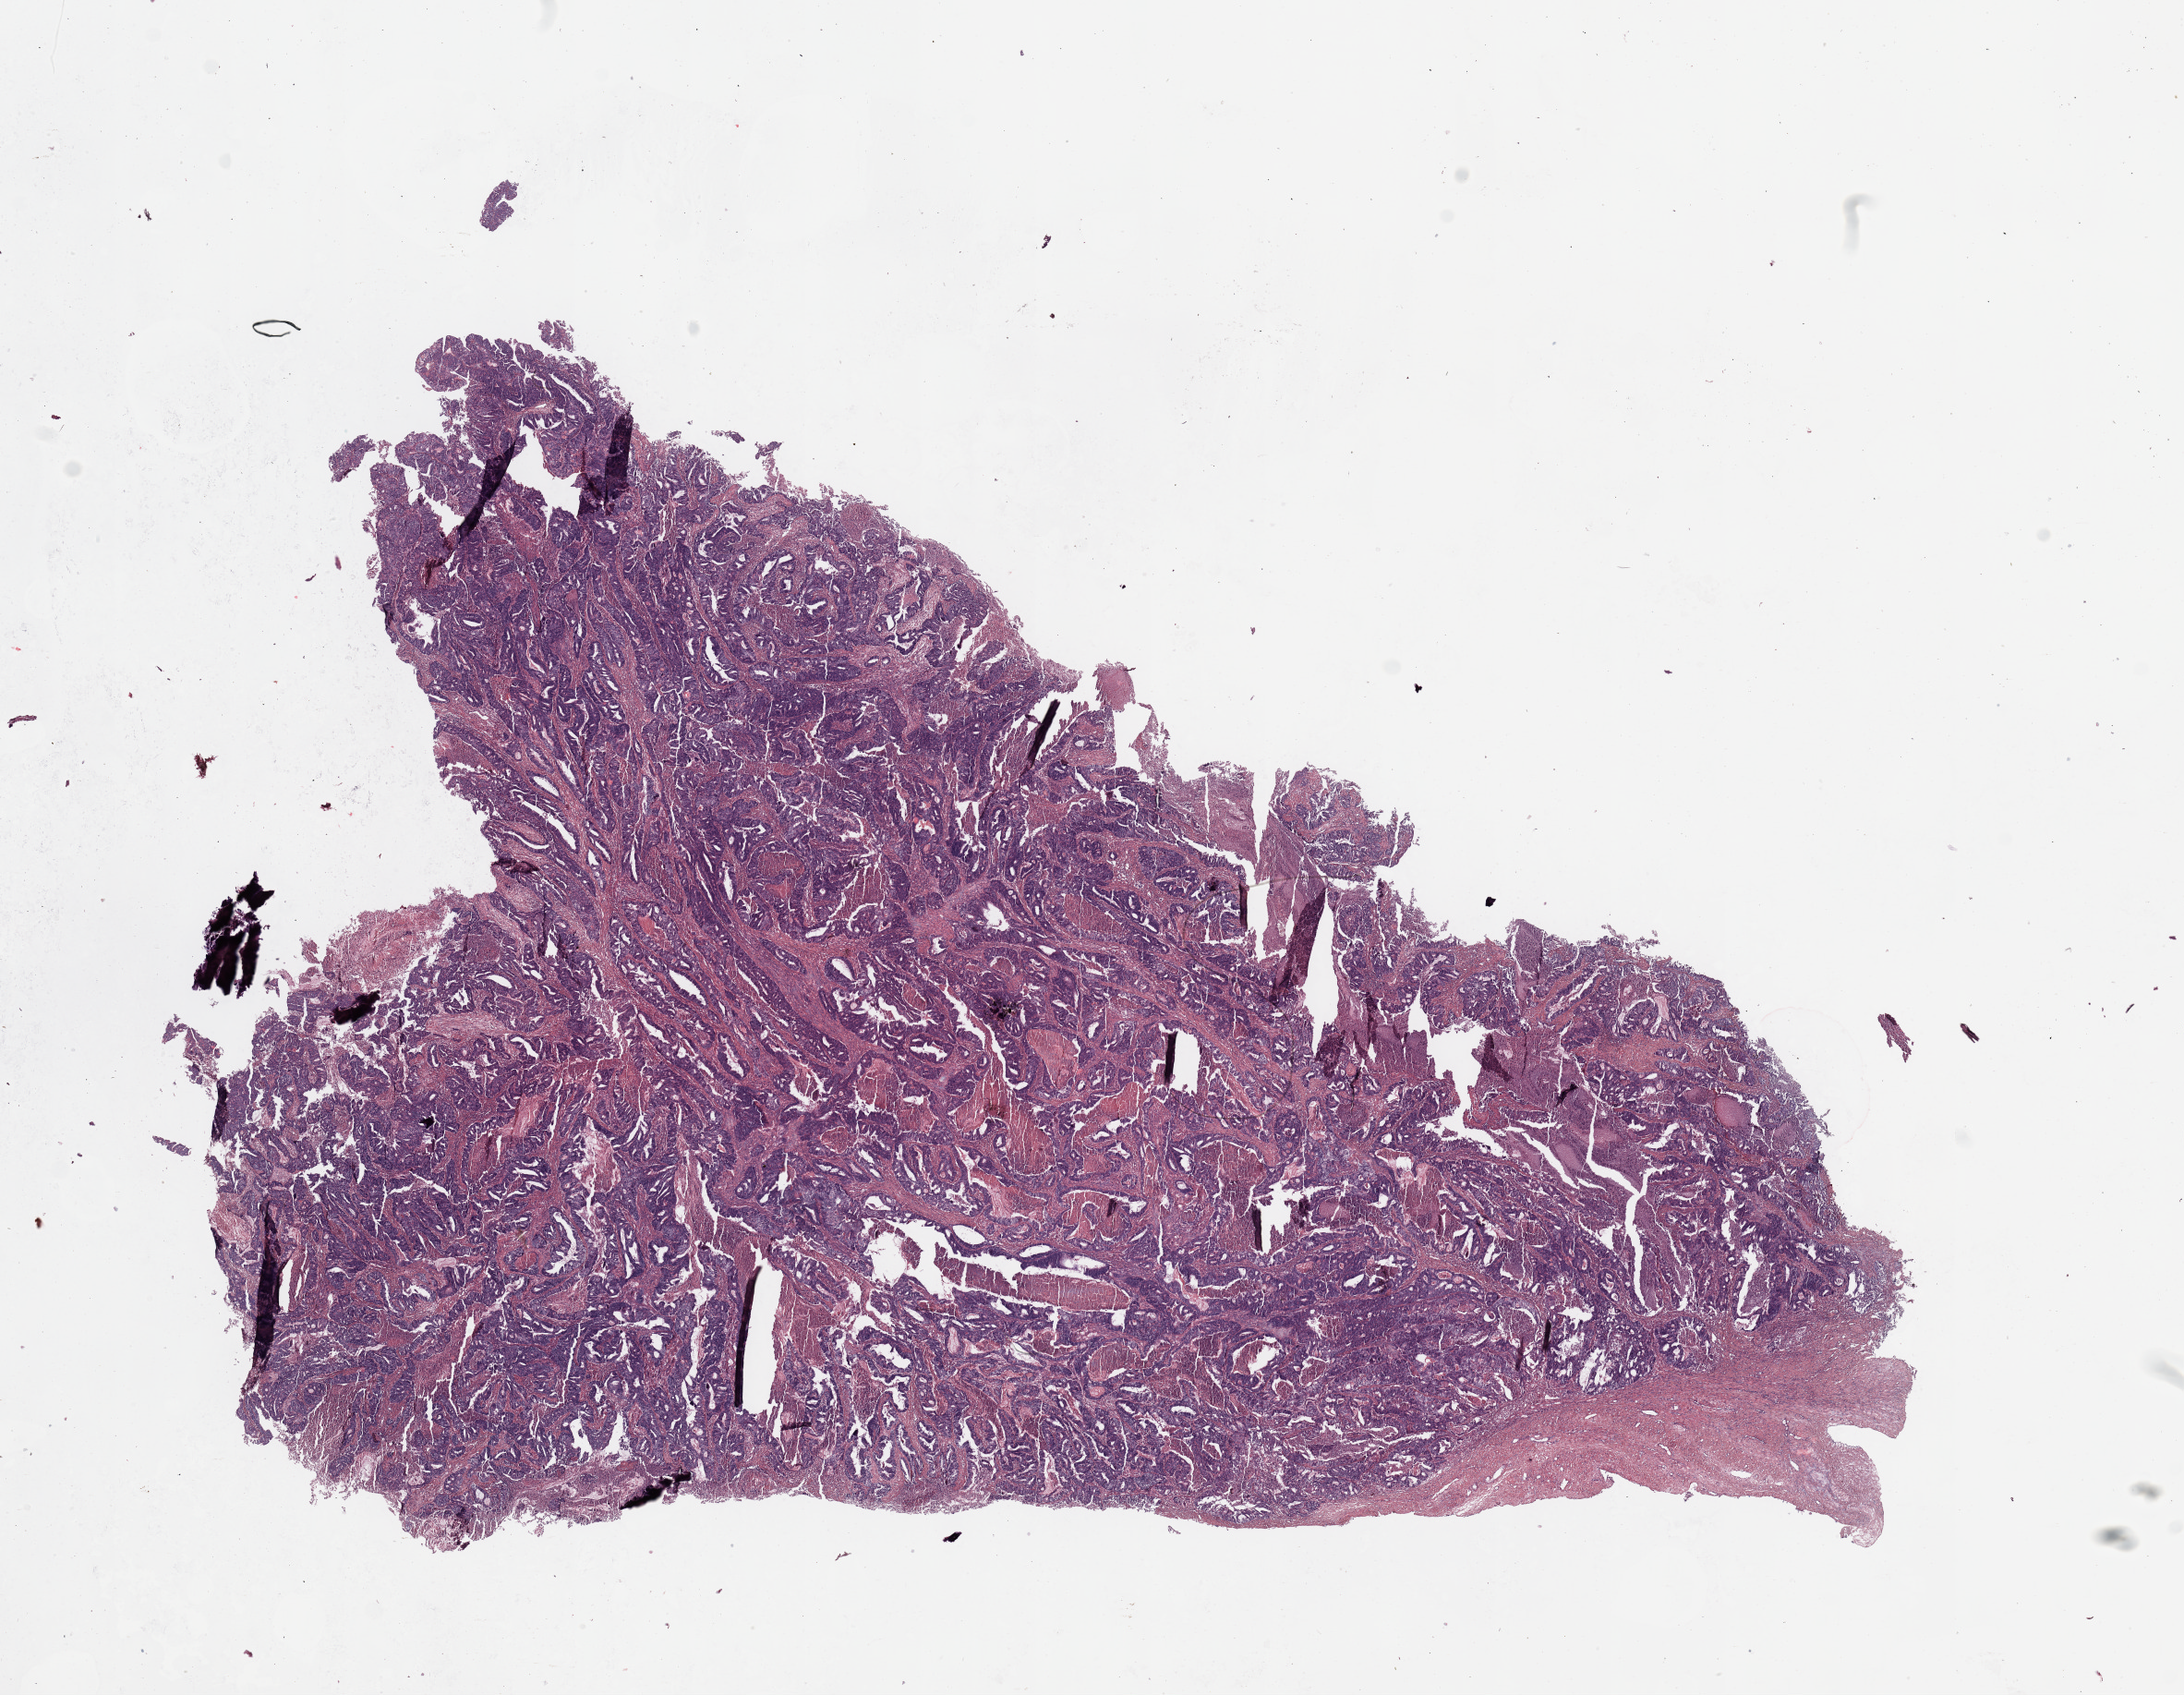
H&E-stained whole-slide image — whole scanned area (about 18.7 x 14.5 mm, slide scanned at 20x) shown as a low-resolution overview; tumour tissue sample, uterus. 62-year-old female patient. Histologic grade: G2 (moderately differentiated).
Diagnosis: Endometrioid adenocarcinoma, NOS. AJCC pathologic stage: I.